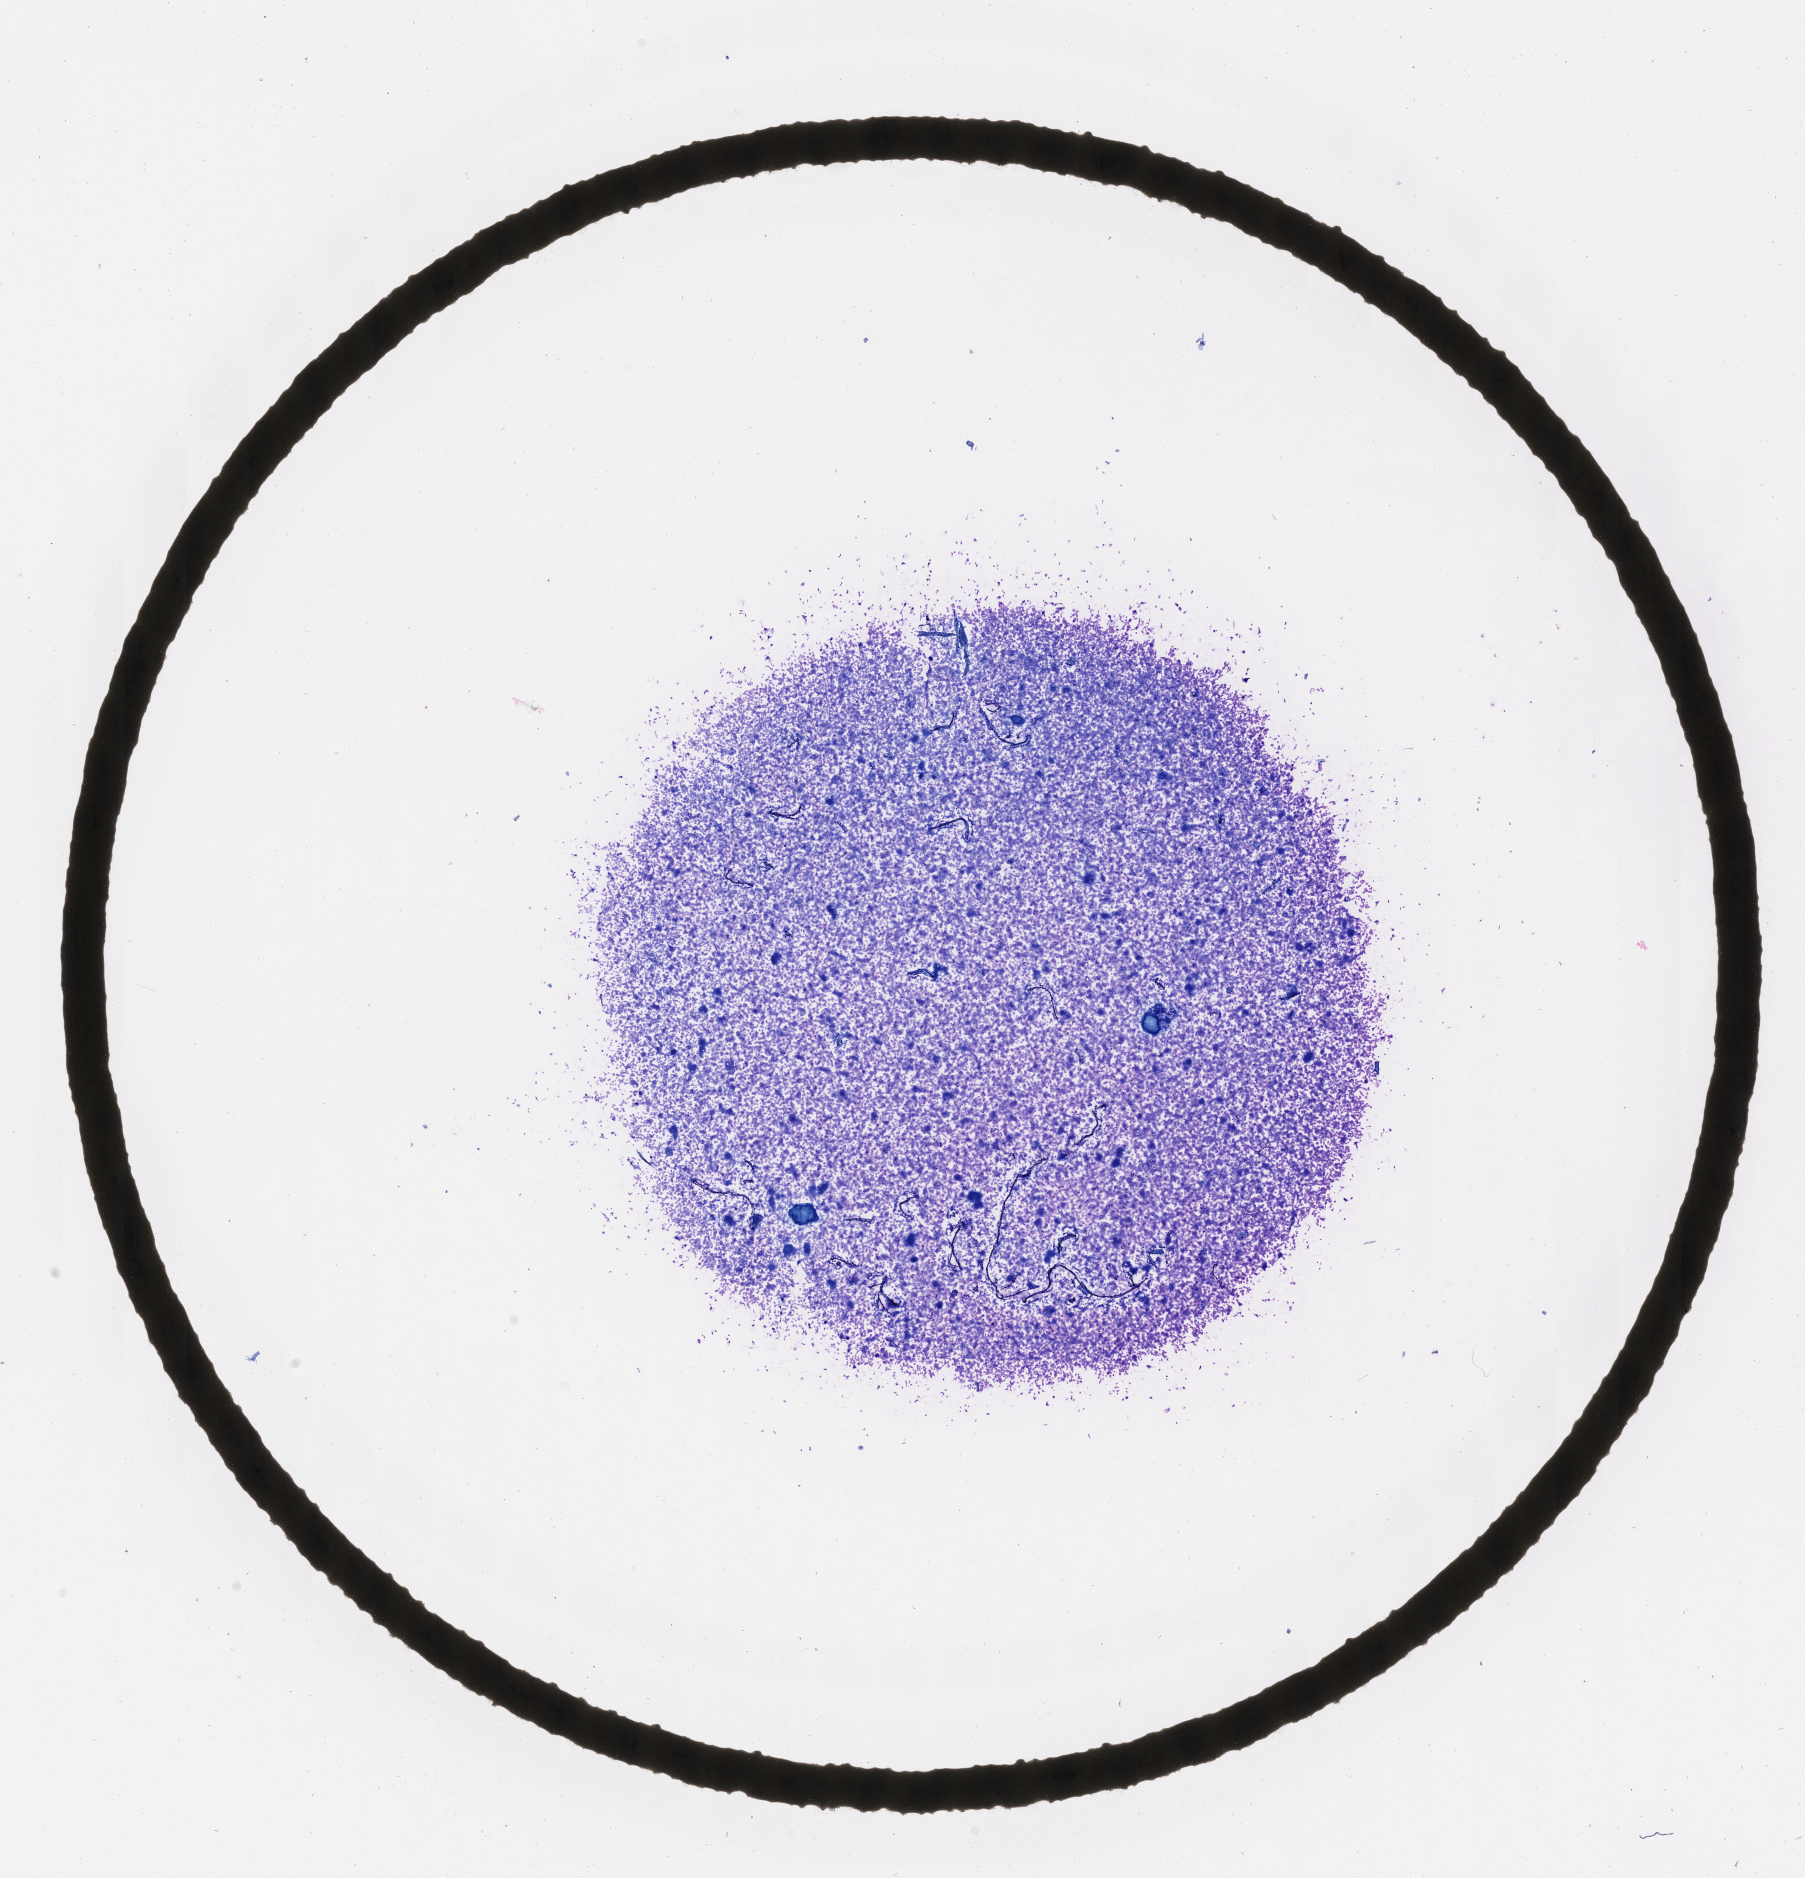
Wright–Giemsa whole-slide image — low-resolution overview of the scanned area, about 14.6 x 15.2 mm, frozen section (tissue freezing medium), specimen: primary tumor, site: lymph node of head and neck. Male patient; age at initial diagnosis 3 years. Pathologist review of this section (percent, as recorded): tumor cells 85%, tumor nuclei 90%, stromal cells 5%, necrosis 0%, normal cells 10%. Infiltration values recorded for this section: lymphocyte infiltration 75%, monocyte infiltration 20%, neutrophil infiltration 5%.
* diagnosis: Burkitt lymphoma, NOS
* Ann Arbor stage (patient): Stage III